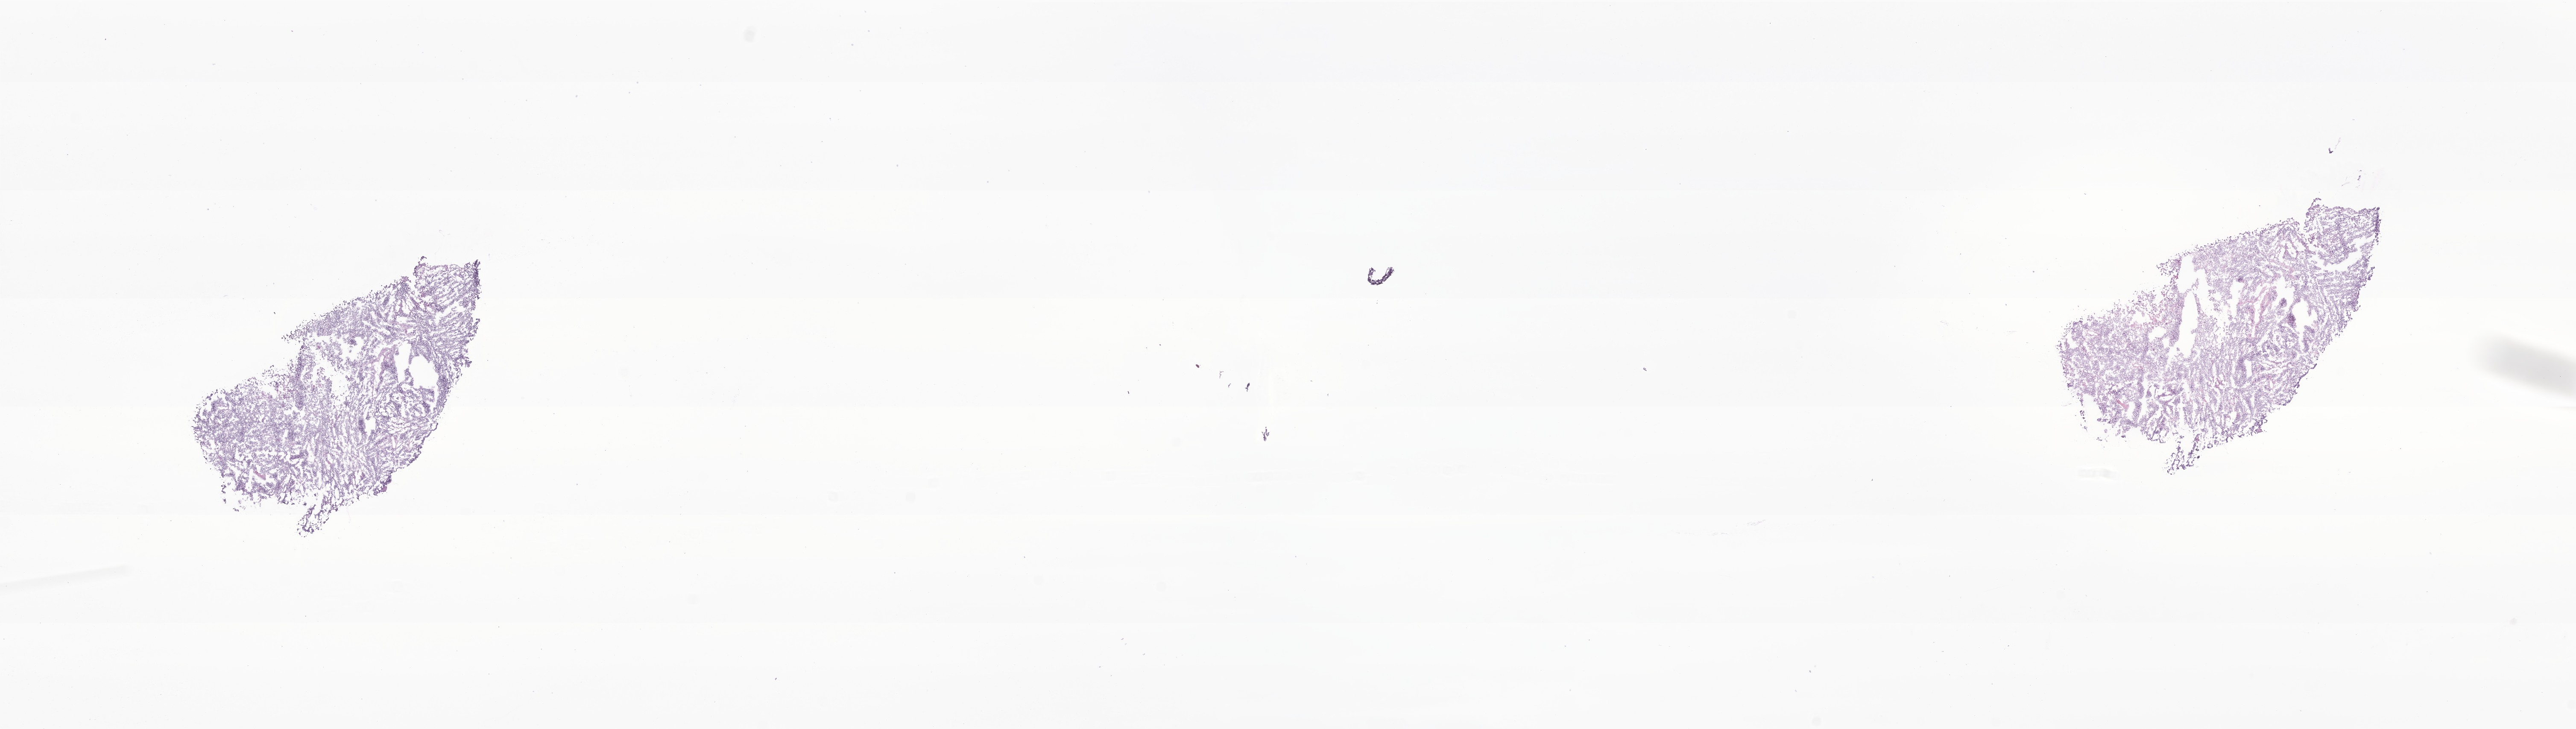
Whole-slide image, H&E stain of tumor tissue from the parietal lobe, a low-resolution overview of the entire scanned area, about 25.4 x 7.2 mm, cryosection (OCT / tissue freezing medium). Patient: male, age 933 days.
Diagnosis: Neoplasm, malignant.